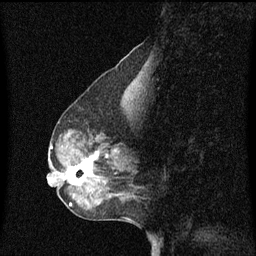
Breast MRI (dynamic contrast-enhanced), one sagittal slice; position 24 of 60 along the scan axis; dynamic contrast-enhanced series, image 2 of 3 at this slice position (ordered by acquisition); 1.5 T; TE 4.2 ms, TR 8.4 ms; 2 mm slice thickness; 256 × 256 image matrix, field of view 200 × 200 mm. Female patient, age 50 years. From the clinical record (not read from this slice): setting: breast cancer imaged before/during neoadjuvant chemotherapy; receptor status: HR-positive, HER2-negative.
Annotated regions visible in this slice (semi-automatic segmentation, software-assisted and operator-edited):
- analysis volume of interest (the breast-tissue region the enhancement analysis was run in; not a lesion): box from (x=61, y=144) to (x=128, y=189) px
- tumour enhancement mask (voxels above the 70 % enhancement threshold inside the analysis volume of interest): (x=68, y=152)–(x=100, y=185)